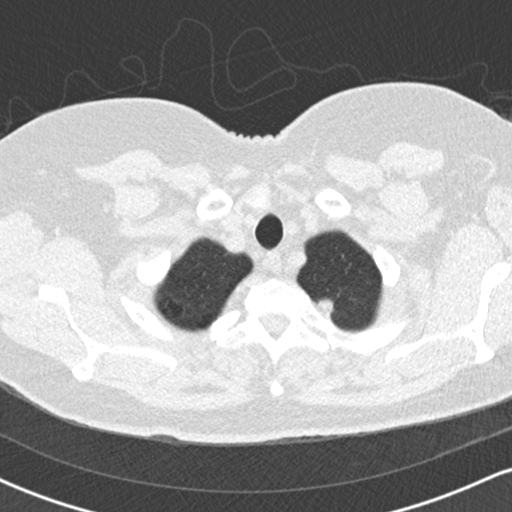
Low-dose screening chest CT, one axial slice; slice 153 of 170 in the series (ordered by position); 120 kVp; lung window (W 1500 / L -600 HU); 2 mm slice thickness; 512 × 512 image matrix, field of view 320 × 320 mm.
Structures marked on this image (expert manual segmentation):
- lesion 1 (tumor, upper lobe of left lung): bounding box [x1, y1, x2, y2] px = [317, 300, 333, 317]